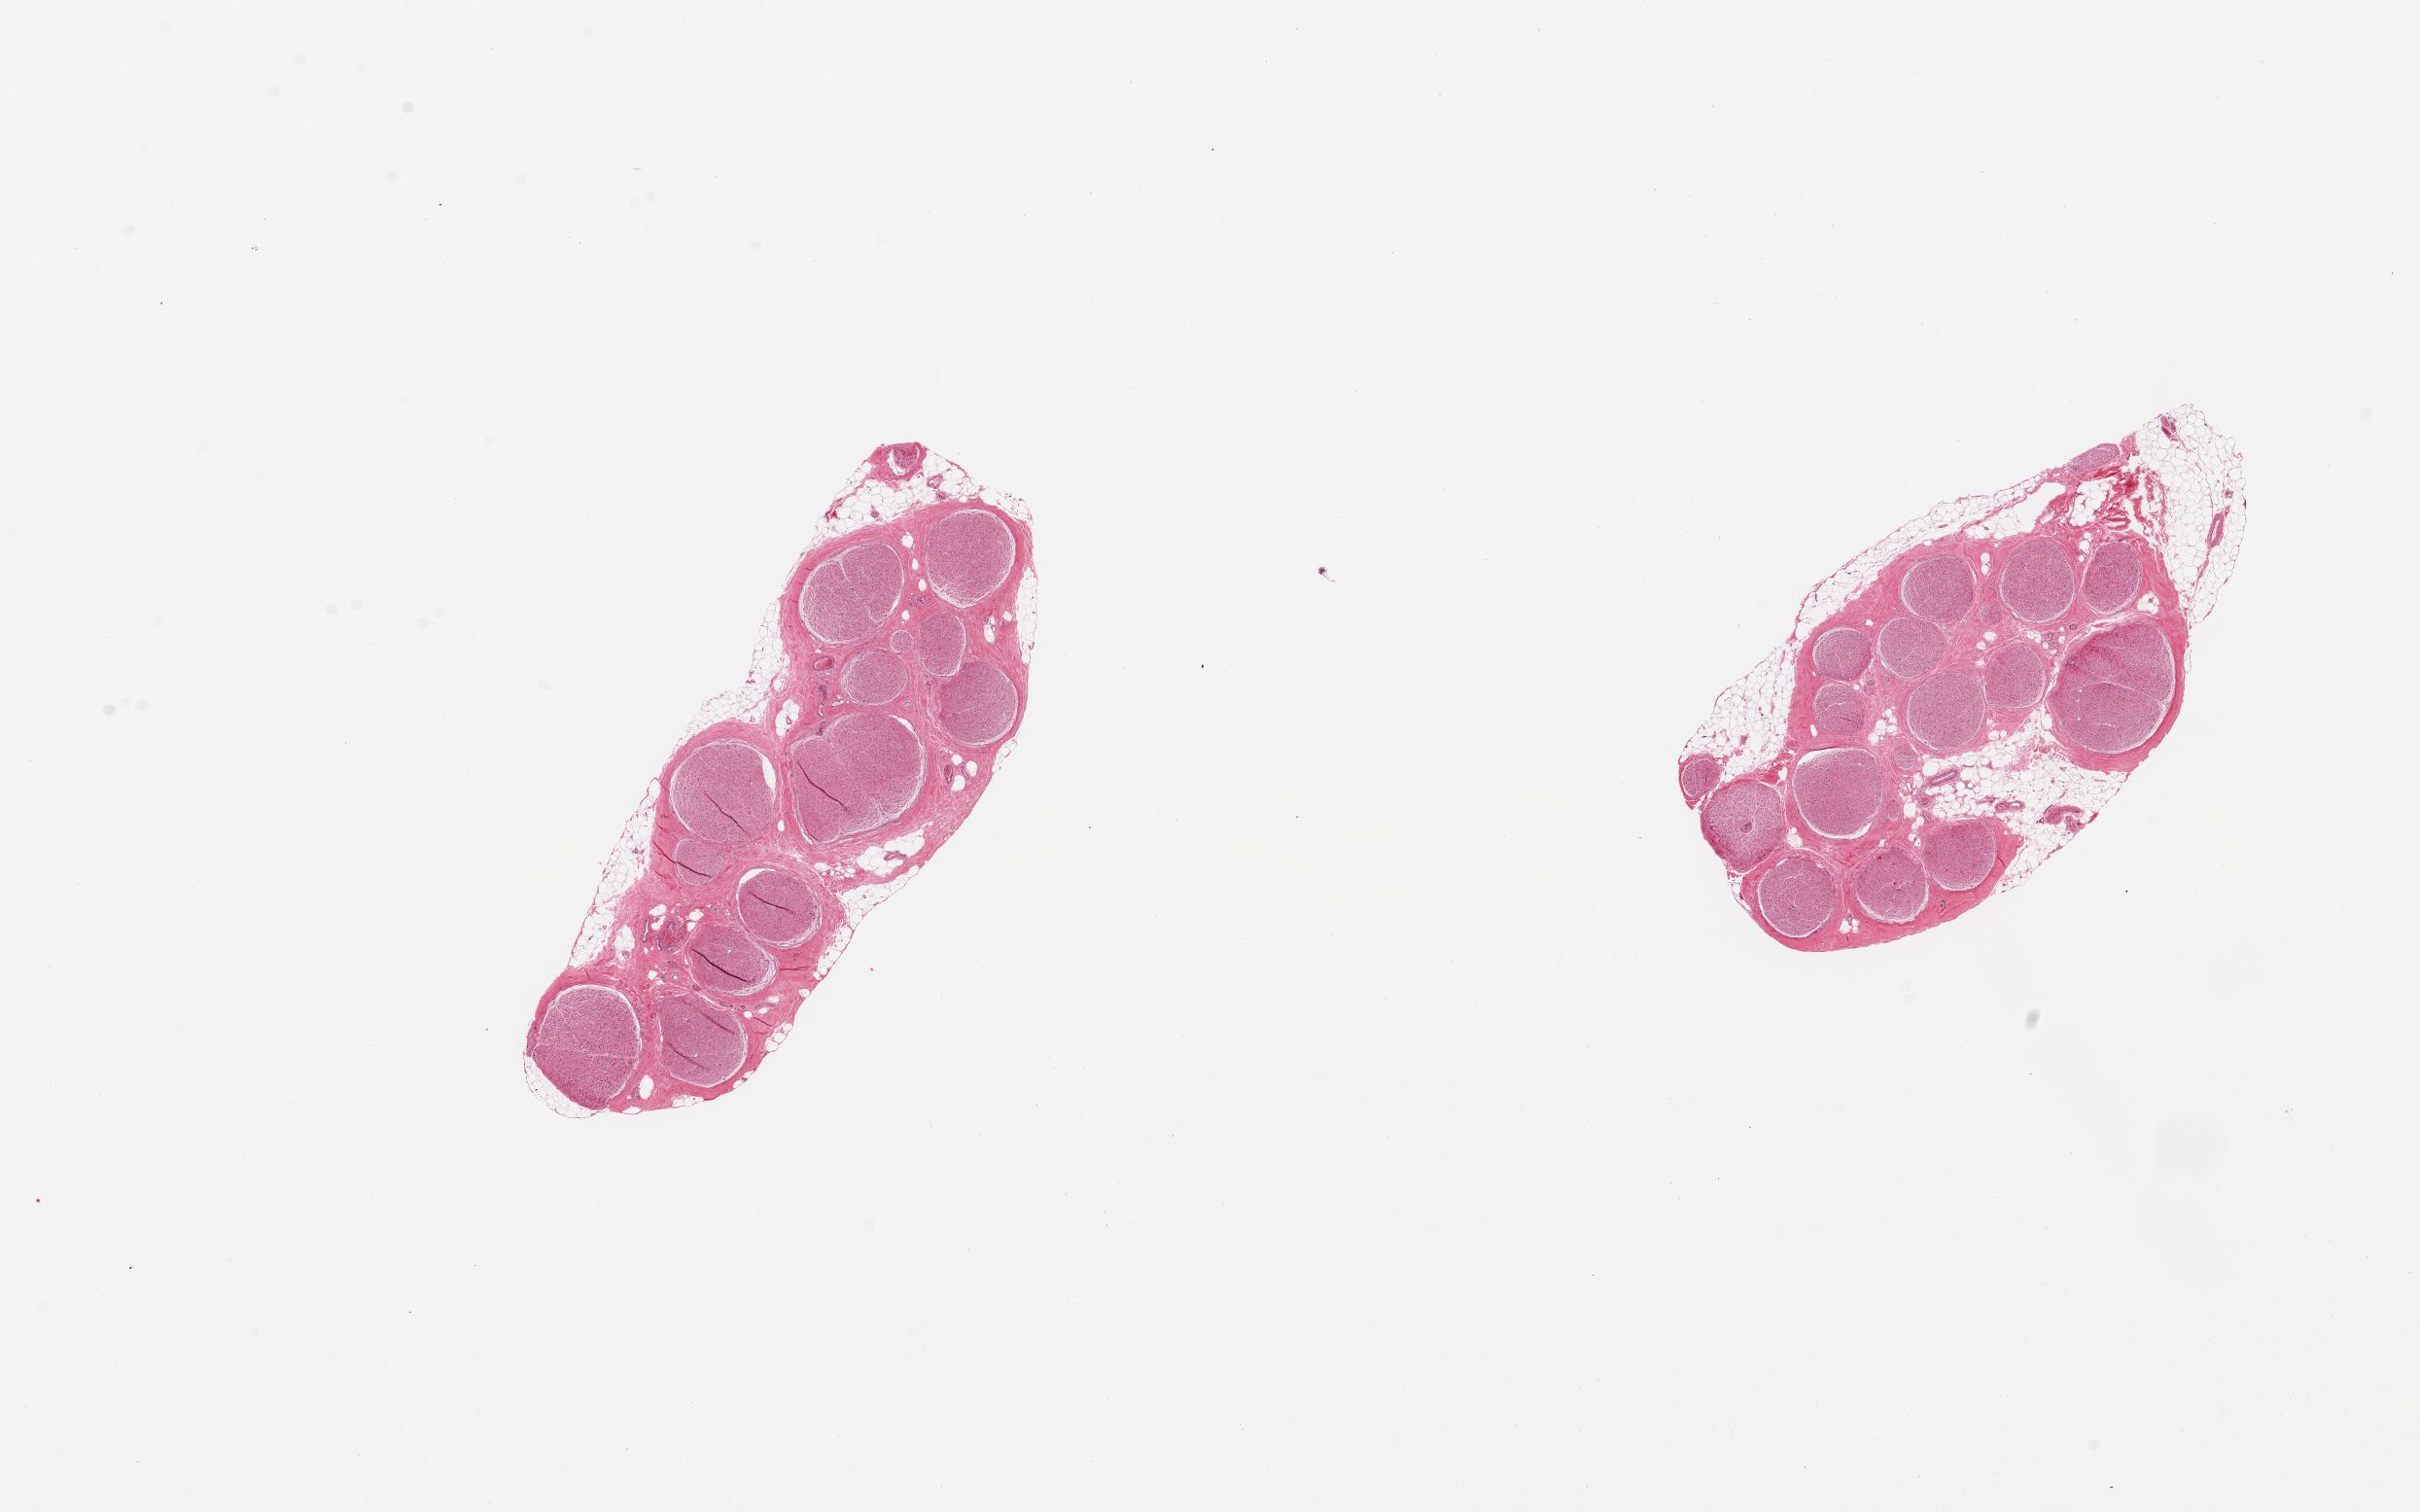
Digitized hematoxylin and eosin (H&E)-stained section, brightfield, whole scanned area (about 19.7 x 12.3 mm, from a 20x scan) shown as a low-resolution overview. PAXgene-fixed paraffin-embedded (PFPE) section. Sampled site (target tissue): tibial nerve. Tissue donor sample.
Reviewer comment on this tissue sample: 2 pieces; 10% external fat.